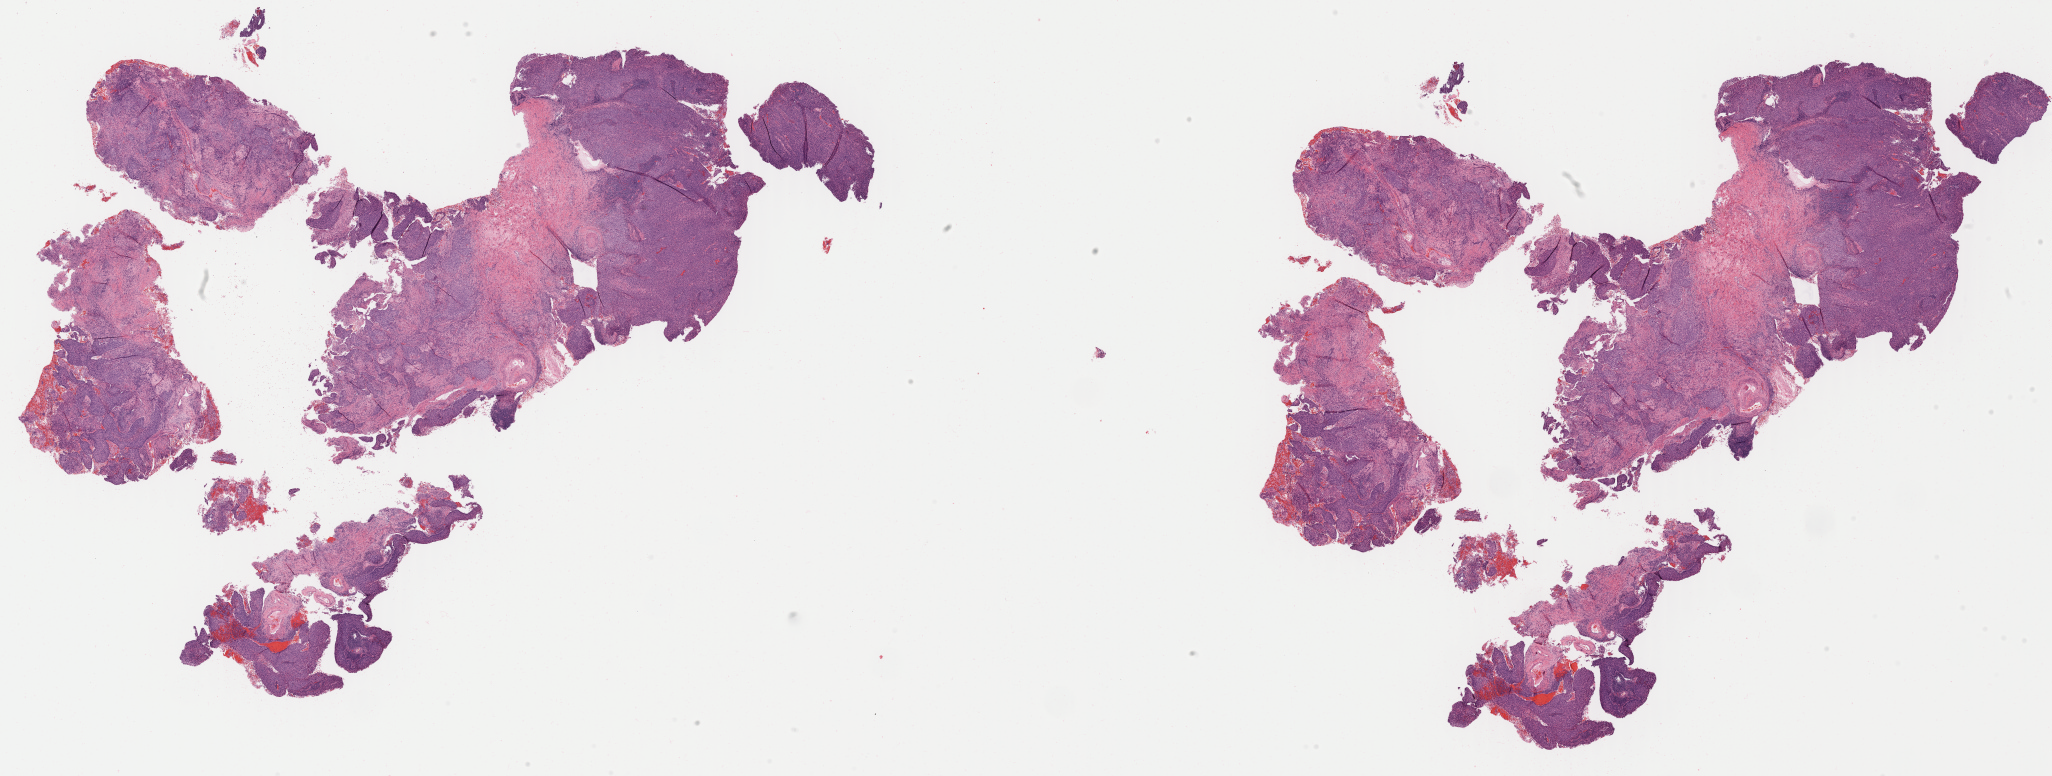
Digitized haematoxylin and eosin-stained section, shown as a low-resolution overview of the whole scanned area (about 32.7 x 12.4 mm); tumor tissue; anatomic site: cervix. Female patient, aged 62.
* diagnosis: Squamous cell carcinoma, large cell, nonkeratinizing, NOS